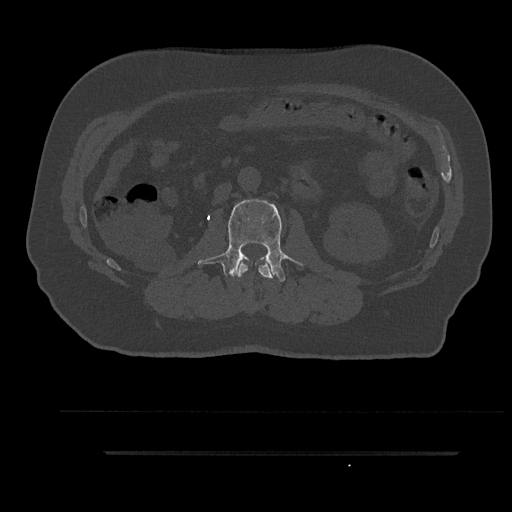
CT including the spine, one axial slice; slice 122 of 797 in the series (ordered by position); reconstruction kernel Br40s/3; bone window (W 1800 / L 400 HU); 0.5 mm slice thickness; 512 × 512 image matrix. Patient: male, 63 years. From the clinical record (not read from this slice): primary cancer: renal.
Outlined on this slice (semi-automatic segmentation, software-assisted and operator-edited):
- L1 vertebra: bounding box <238,259,274,279> (left, top, right, bottom; pixels)
- L2 vertebra: <198,199,302,282>